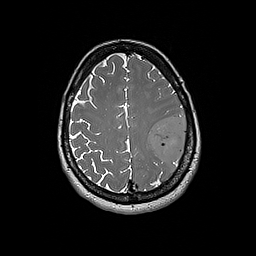
Brain MRI from a brain-tumour surgery series, one axial slice. Slice 63 of 192 in the series (ordered by position). 1 mm slice thickness. 256 × 256 image matrix, field of view 250 × 250 mm. Case-level facts recorded for this patient, not image findings: histopathology: Glioblastoma; WHO grade: 4; IDH mutation: no.
Structures marked on this image (expert manual segmentation):
- tumour: bounding box <149,114,187,163> (left, top, right, bottom; pixels)